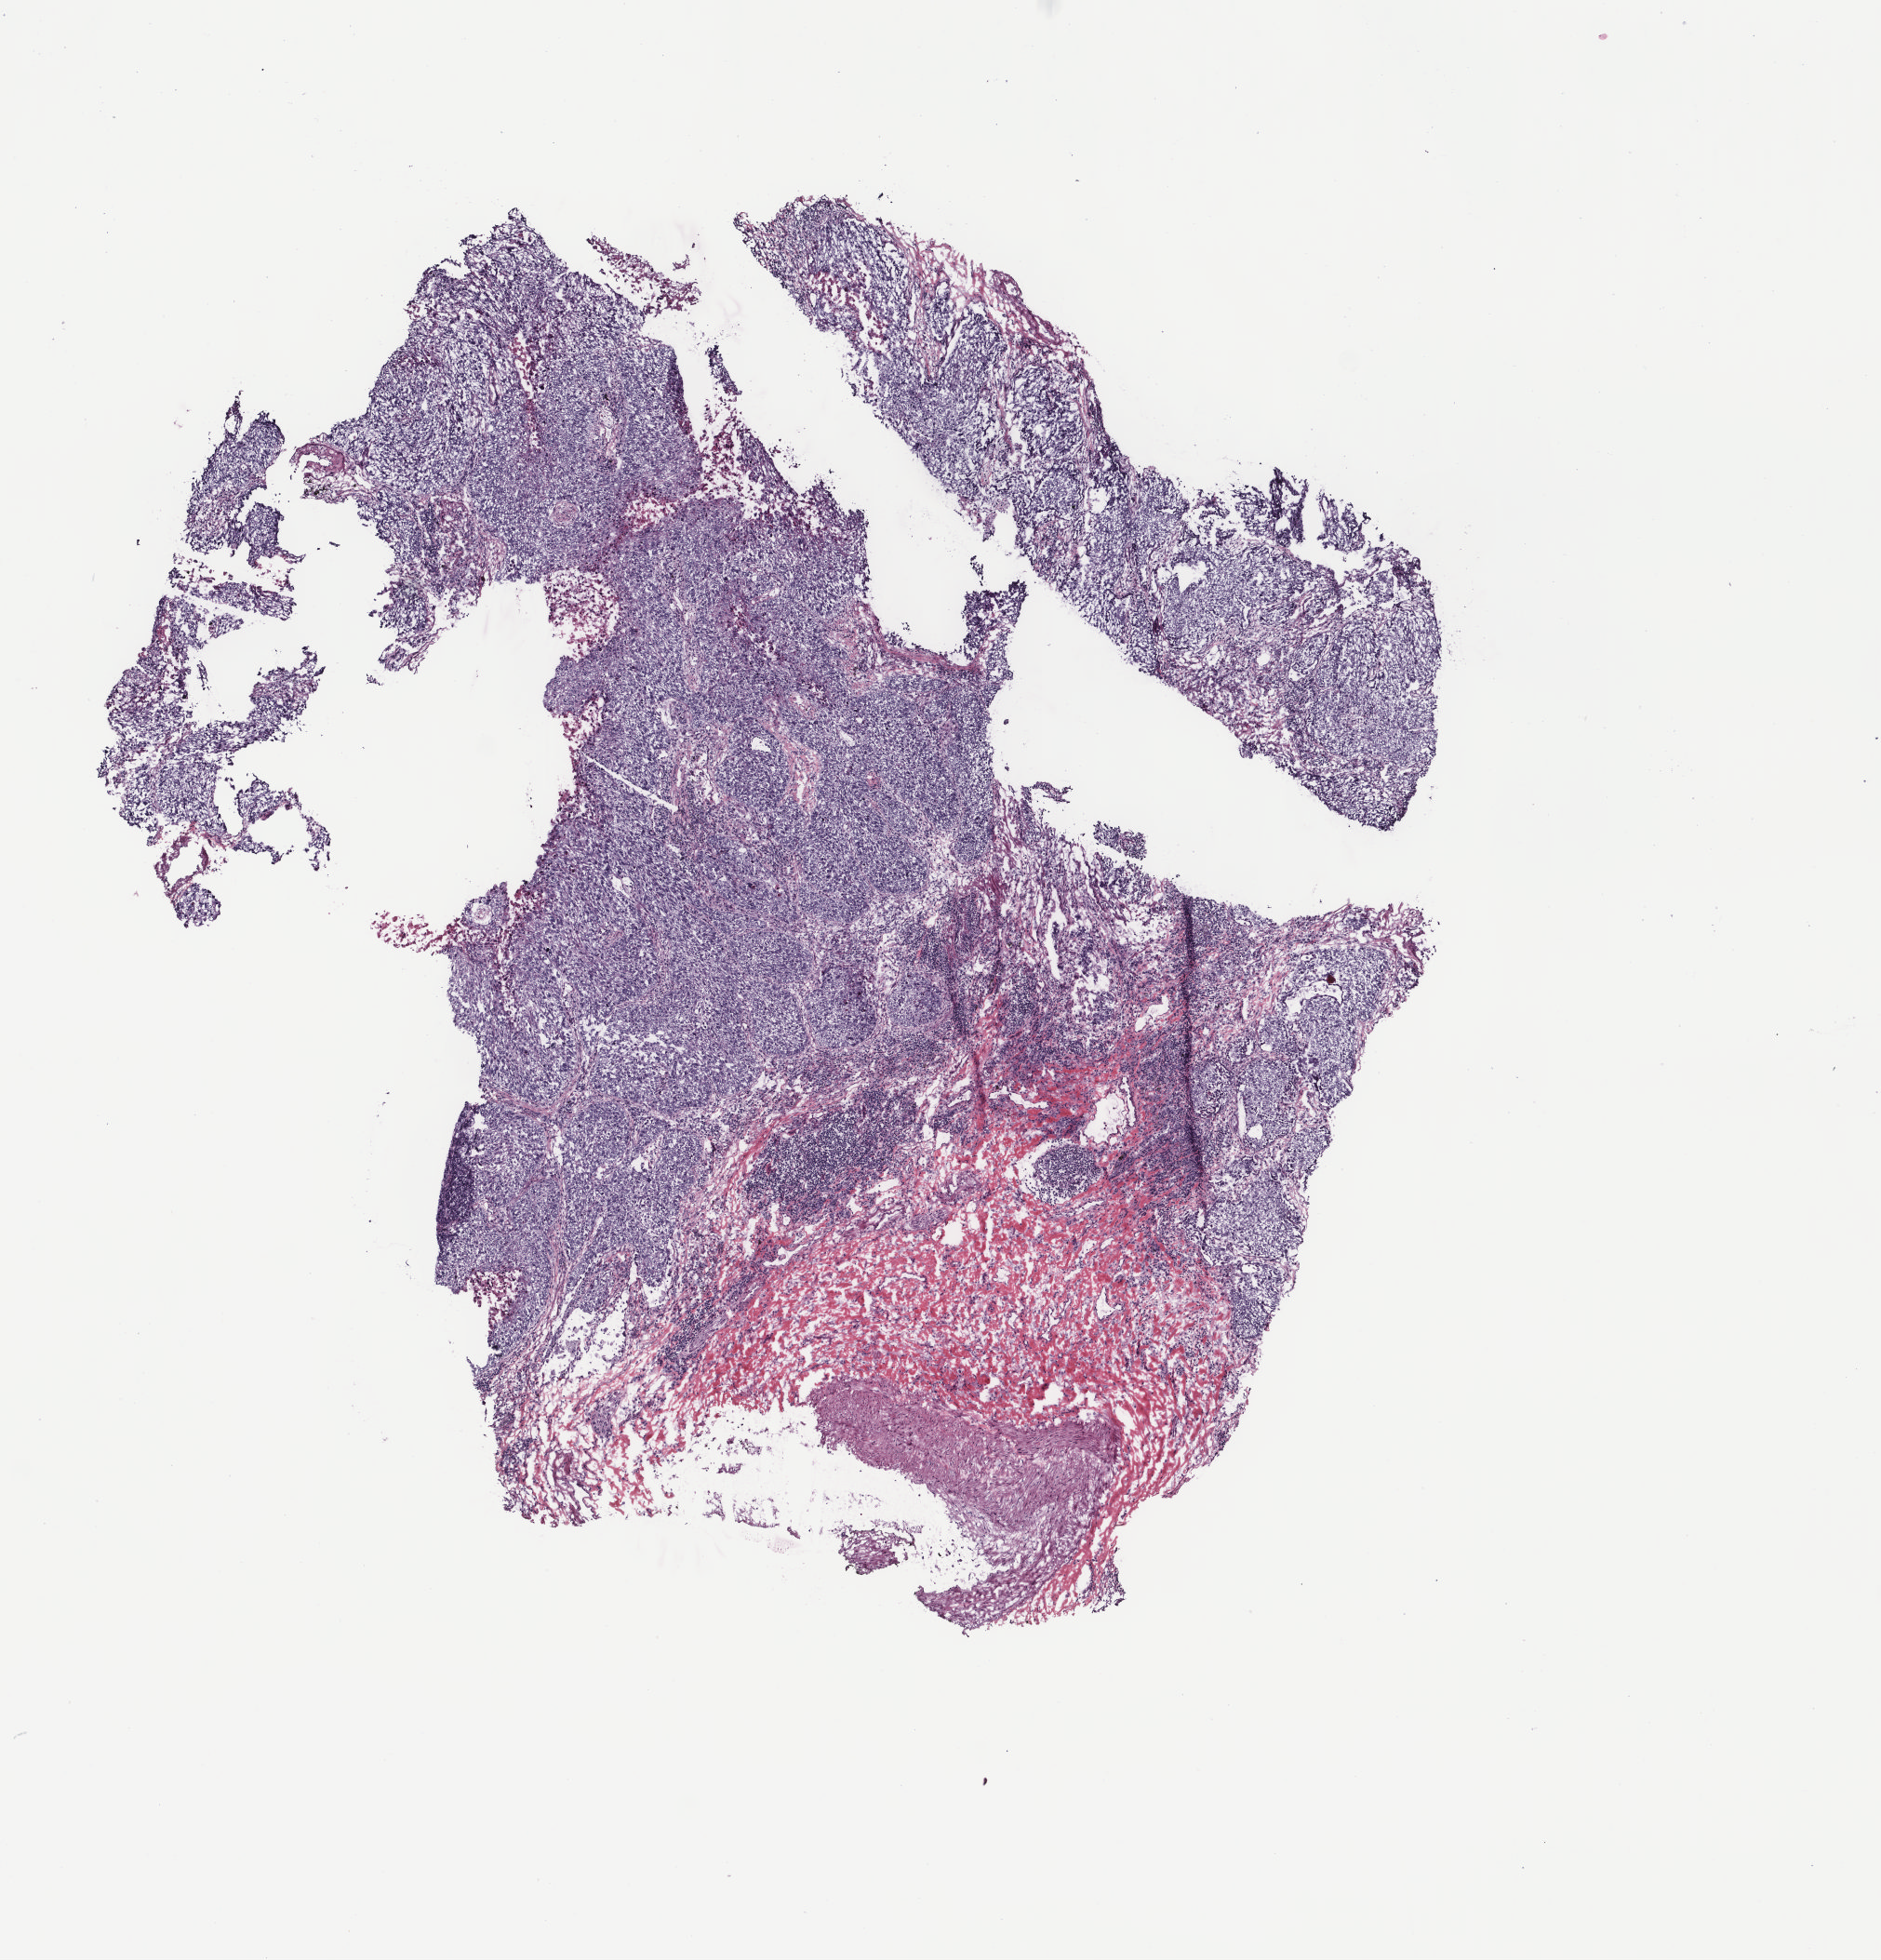
H&E whole-slide image — shown as a low-resolution overview of the whole scanned area (about 8.0 x 8.4 mm, slide scanned at 40x), frozen section from the top of the tissue portion, sample: primary tumour, lung. Male, age 66 years at initial diagnosis. Pathologist review of this section (percent, as recorded): tumour cells 85%, tumour nuclei 90%, normal cells 5%, stromal cells 10%, necrosis 0%. Infiltration values recorded for this section: lymphocyte infiltration 0%, monocyte infiltration 0%, neutrophil infiltration 0%.
• pathologic diagnosis: Squamous cell carcinoma, keratinizing, NOS
• AJCC pathologic stage: IB (7th edition)
• TNM: T2a N0 MX